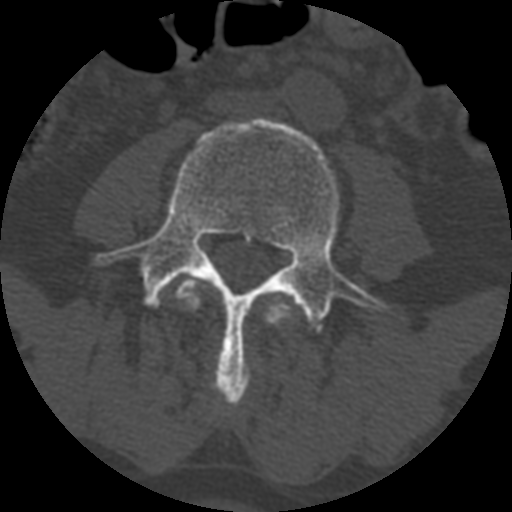
CT including the spine, one axial slice; position 286 of 399 along the scan axis; 120 kVp; bone window (W 1800 / L 400 HU); 512 × 512 image matrix. Patient age 71 years. From the clinical record (not read from this slice): primary cancer: prostate.
Outlined on this slice (semi-automatic segmentation, software-assisted and operator-edited):
- L3 vertebra: box from (x=175, y=279) to (x=295, y=327) px
- L4 vertebra: (x=97, y=119)–(x=388, y=406)